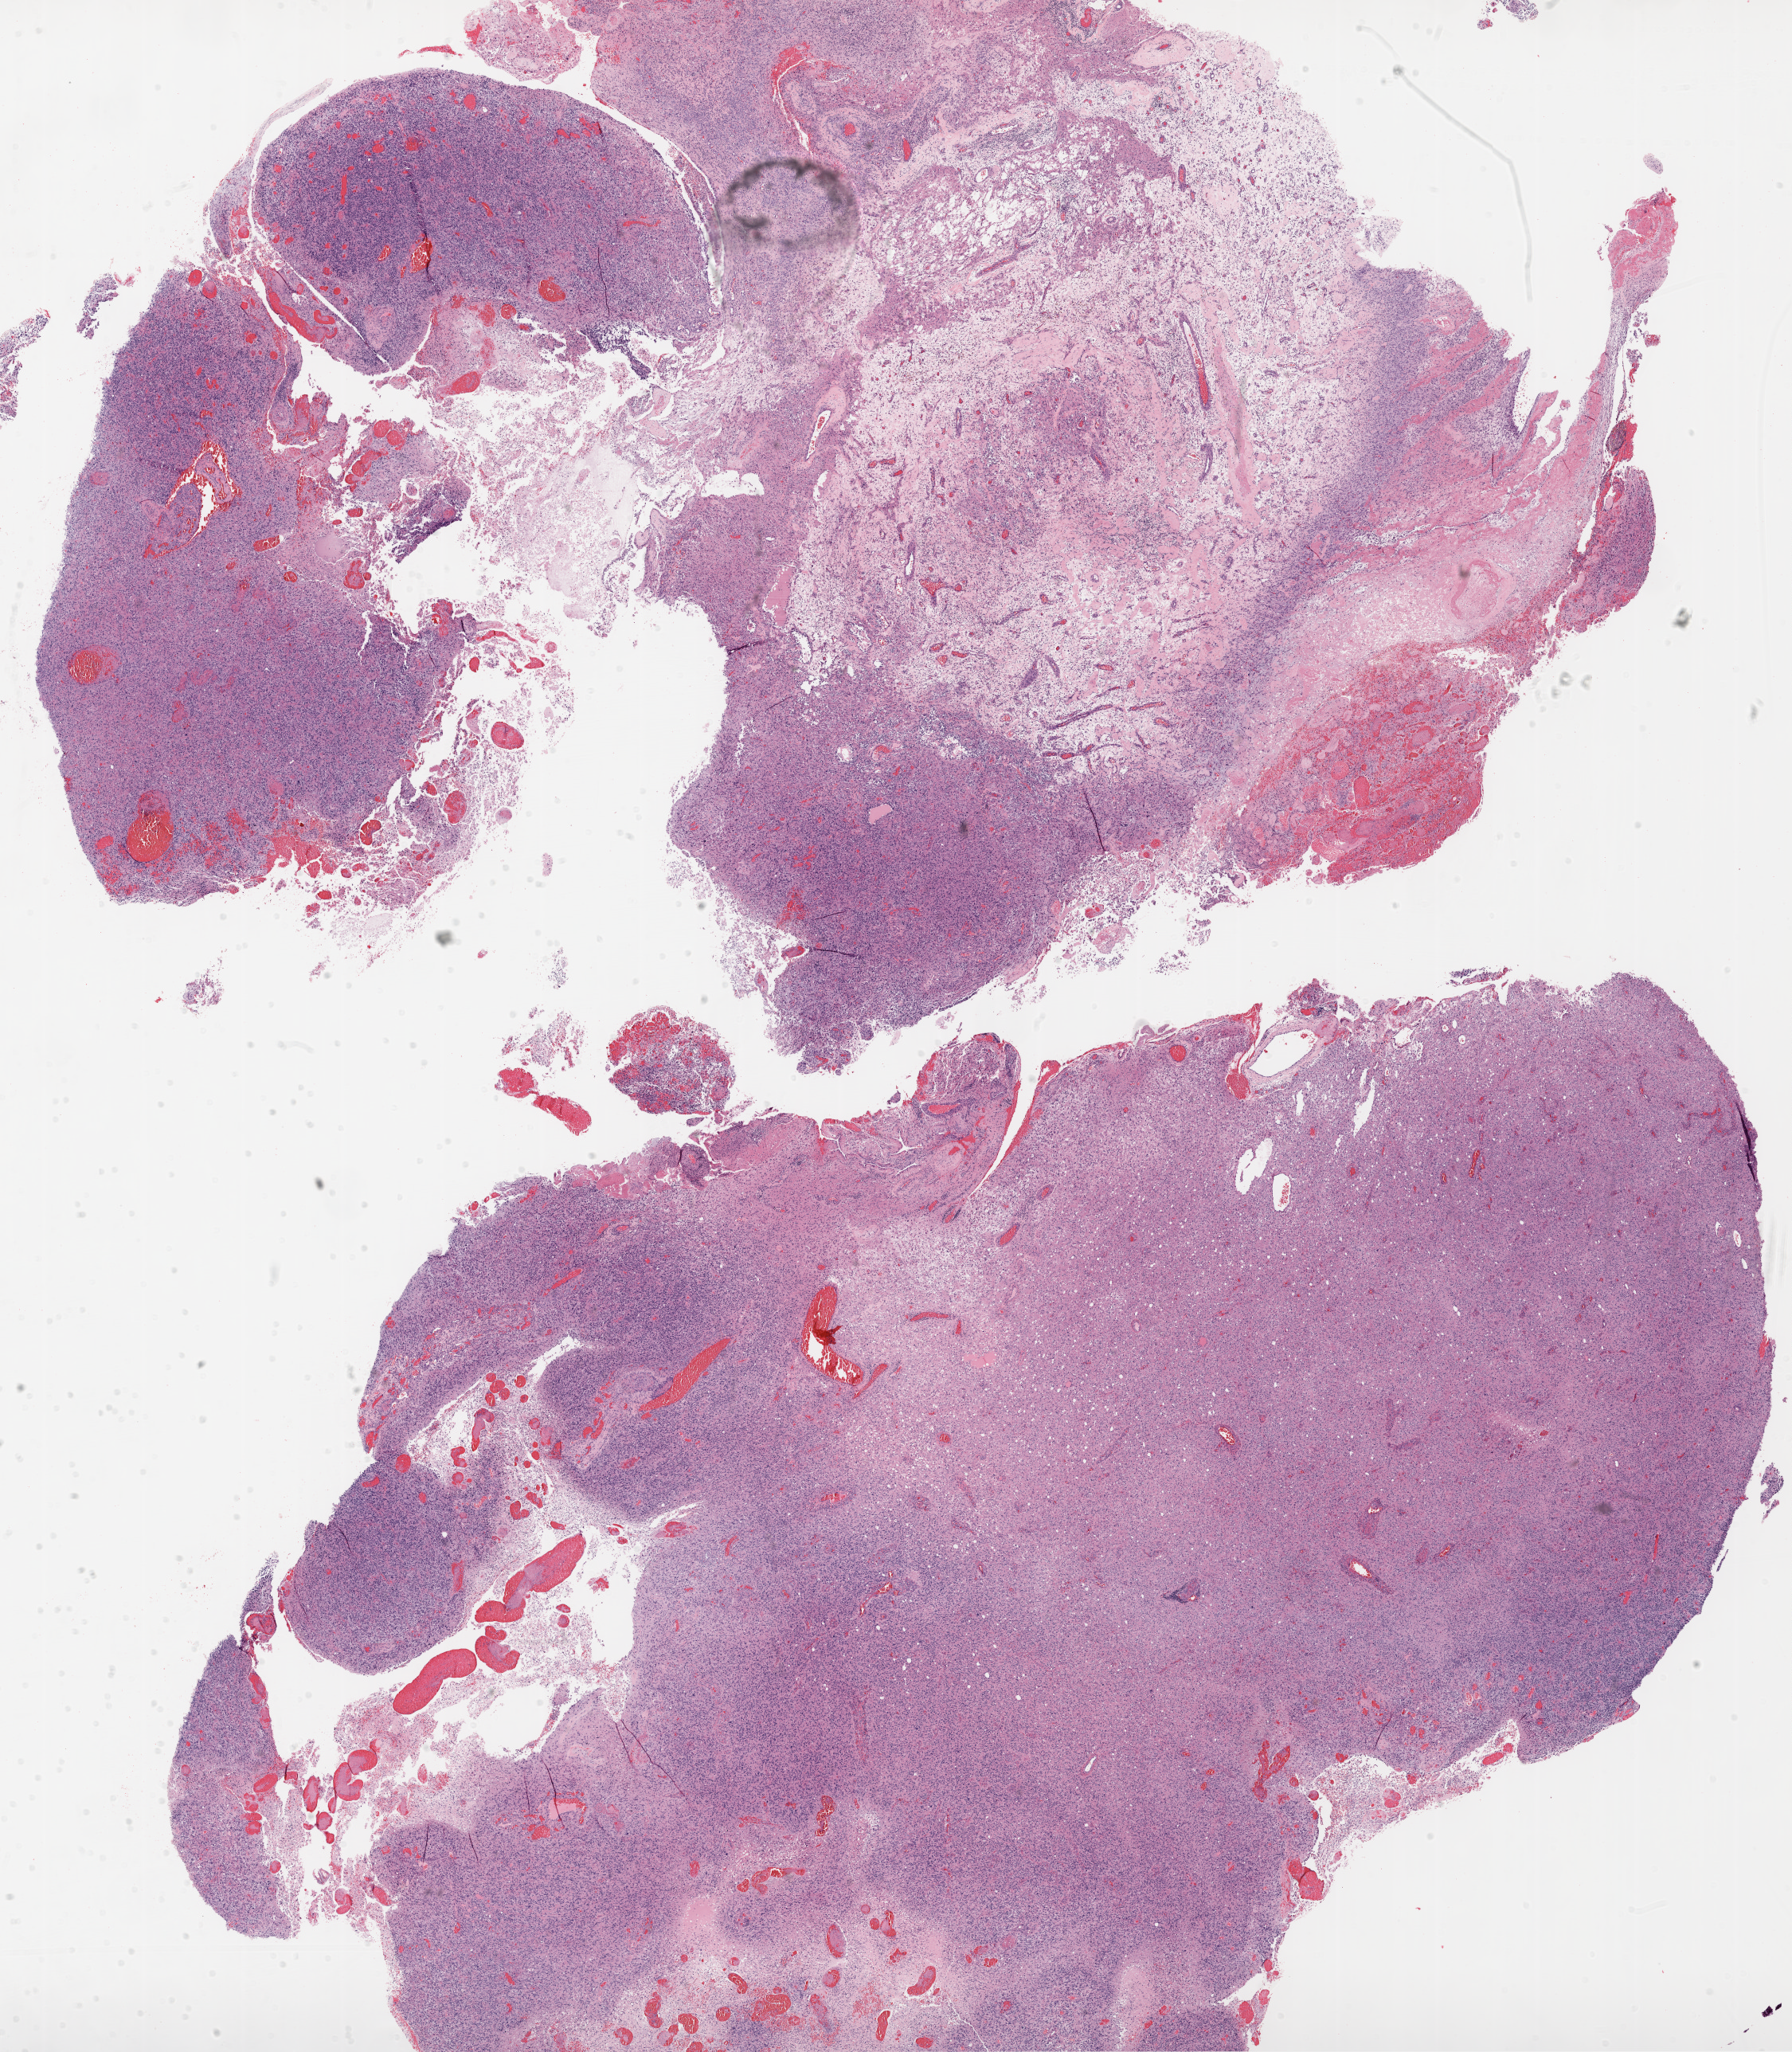
Whole-slide histology image, H&E — whole scanned area (about 18.1 x 20.7 mm) shown as a low-resolution overview. Formalin-fixed paraffin-embedded (FFPE) diagnostic section. Primary tumour sample from the brain. Male, age 39 years at initial diagnosis.
Histologic diagnosis: Glioblastoma.